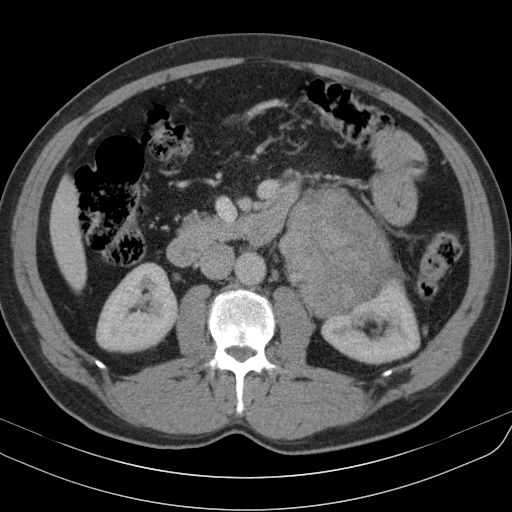
Contrast-enhanced abdominal CT, one axial slice; slice 57 of 91 in the series (ordered by position); 130 kVp; intravenous contrast given; soft-tissue window (W 400 / L 40 HU); 512 × 512 image matrix, field of view 370 × 370 mm. Male patient, age 51 years. Case-level facts recorded for this patient, not image findings: diagnosis: adrenocortical carcinoma; tumour side: left adrenal; tumour size at pathology: 18 cm; Ki-67 index: 40 %; stage (as recorded): 3.
Outlined on this slice (semi-automatic segmentation, software-assisted and operator-edited):
- mass: bounding box <286,191,395,317> (left, top, right, bottom; pixels)